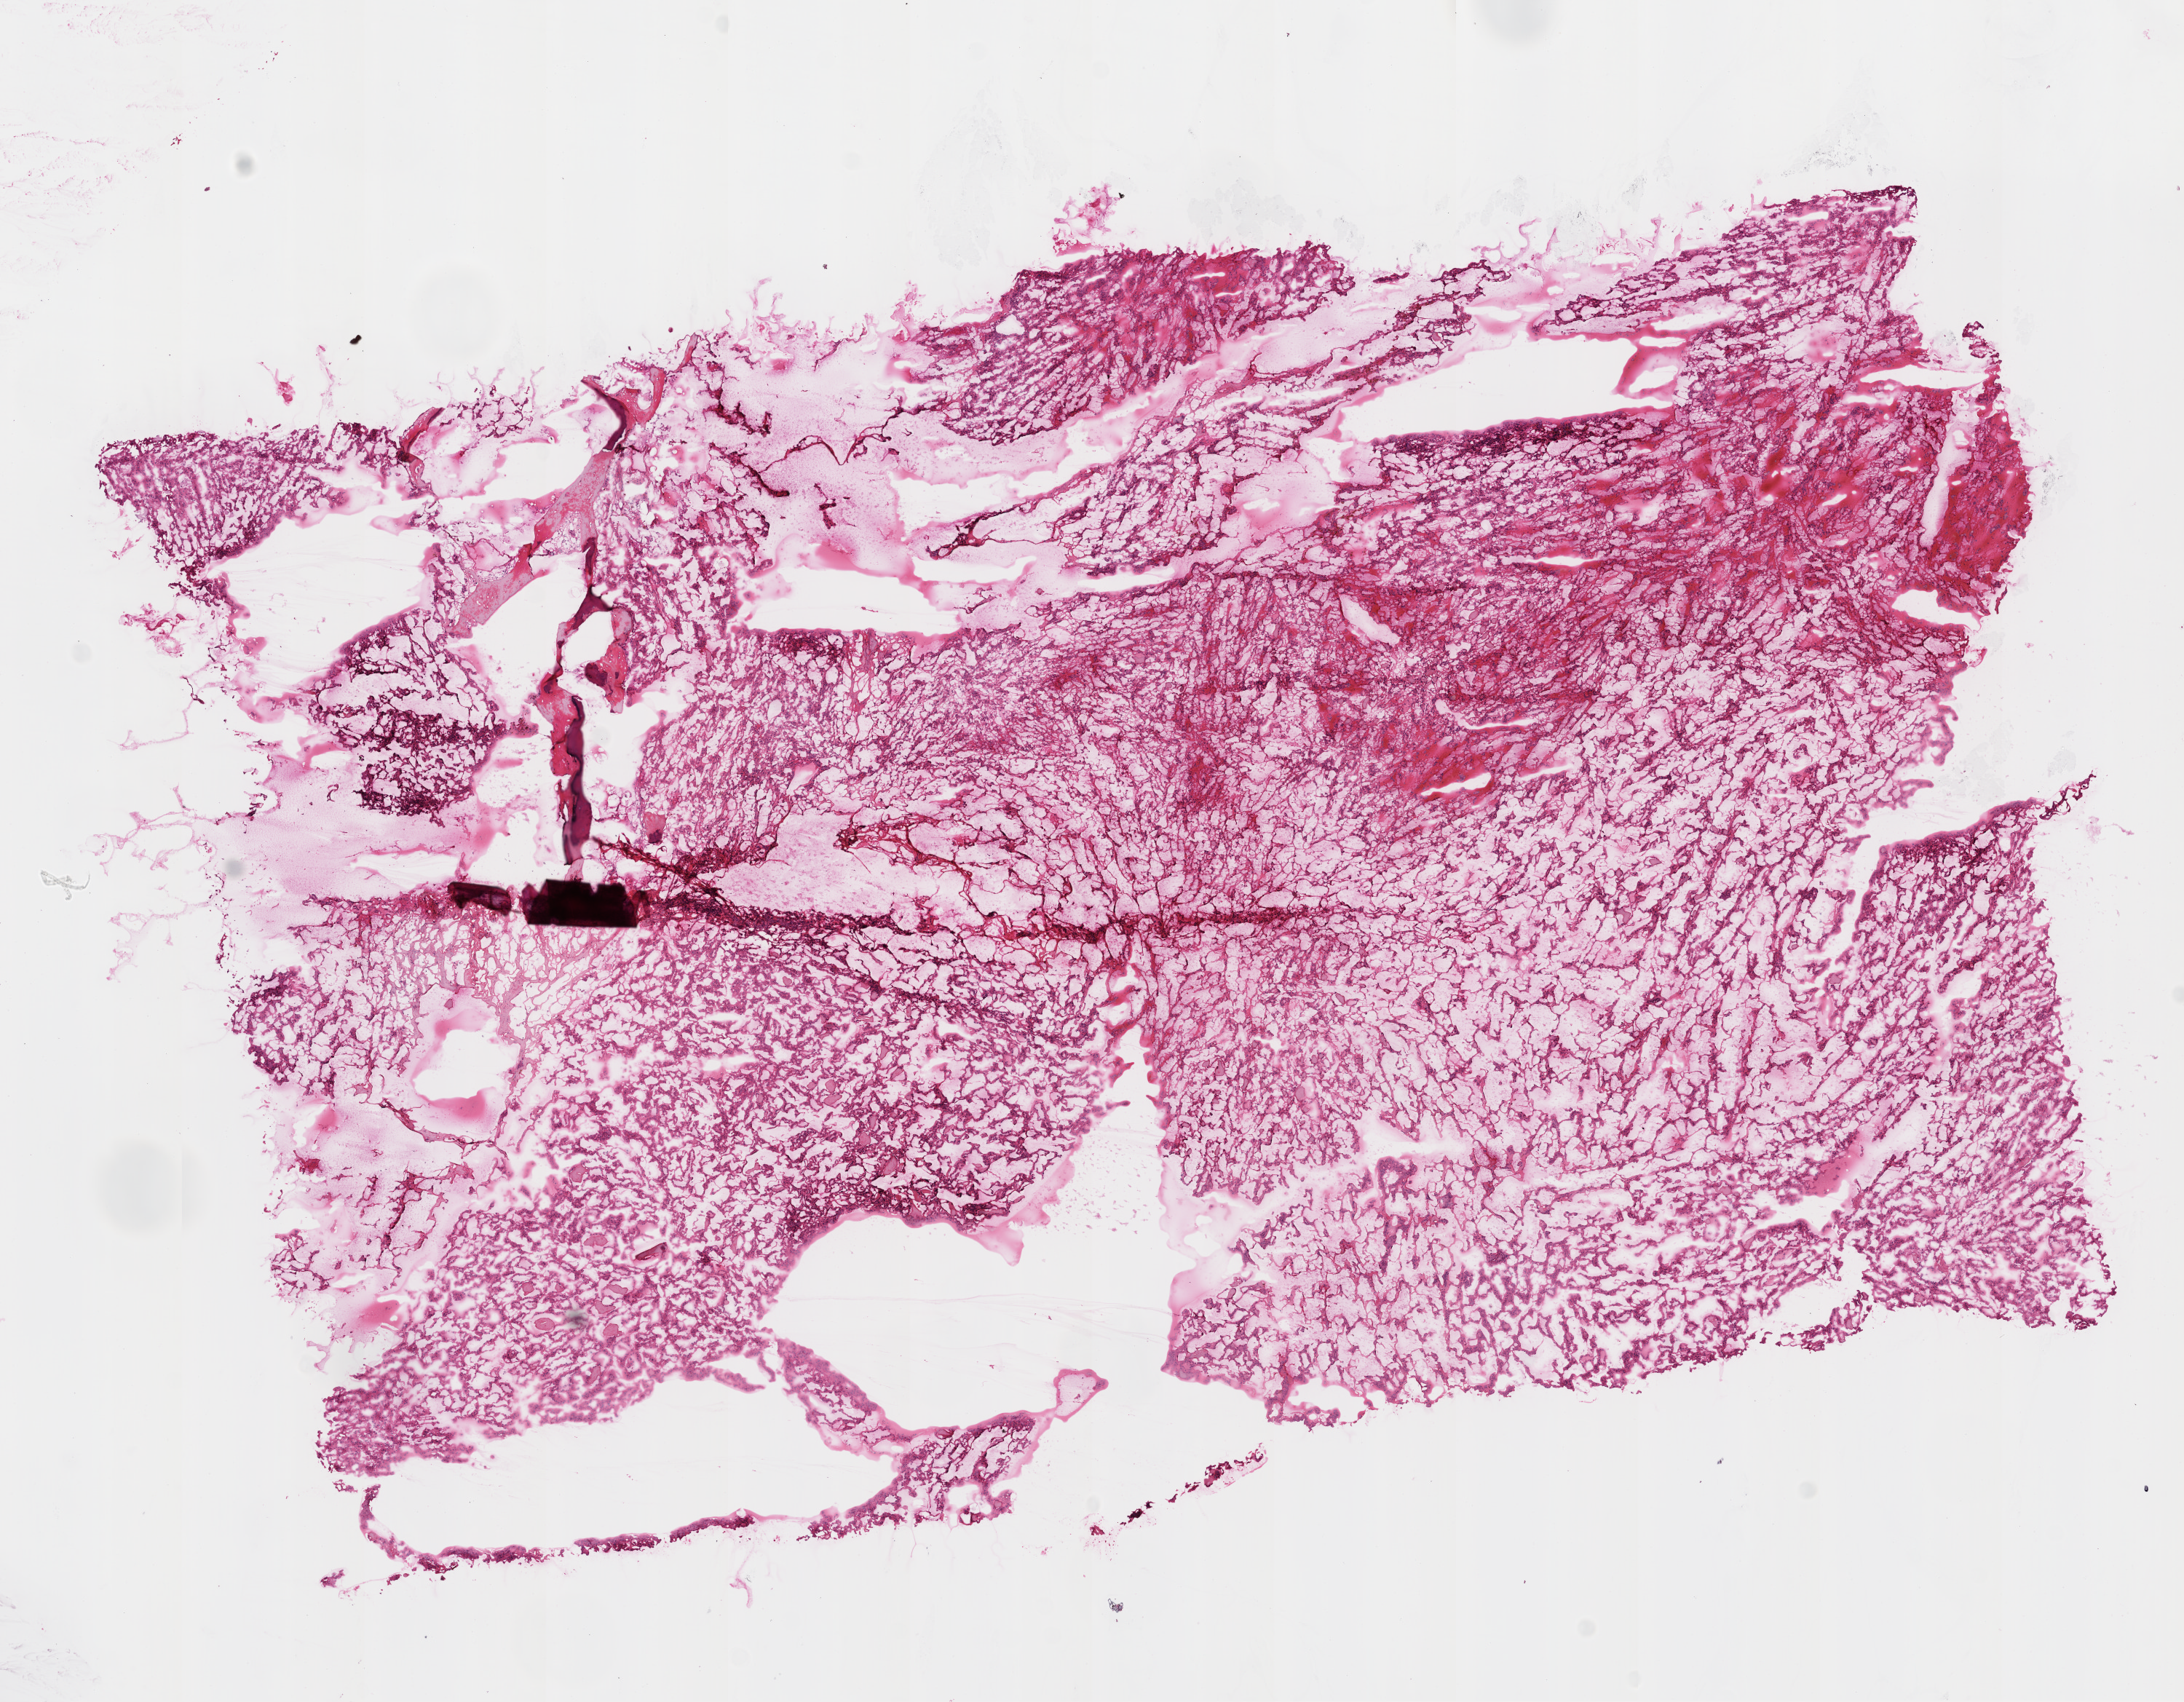
Digitized Hematoxylin and eosin (H&E) stained tissue section (whole slide) — low-resolution overview of the scanned area, about 12.0 x 9.4 mm (slide scanned at 20x), frozen section from the top of the tissue portion, sample: primary tumour, kidney. Female, age 58 years at initial diagnosis. Histologic grade: G2 (moderately differentiated). Pathologist review of this section (percent, as recorded): tumour cells 95%, tumour nuclei 85%, normal cells 0%, stromal cells 5%, necrosis 0%.
• pathologic diagnosis: Clear cell adenocarcinoma, NOS
• AJCC pathologic stage: II (6th edition)
• laterality: right